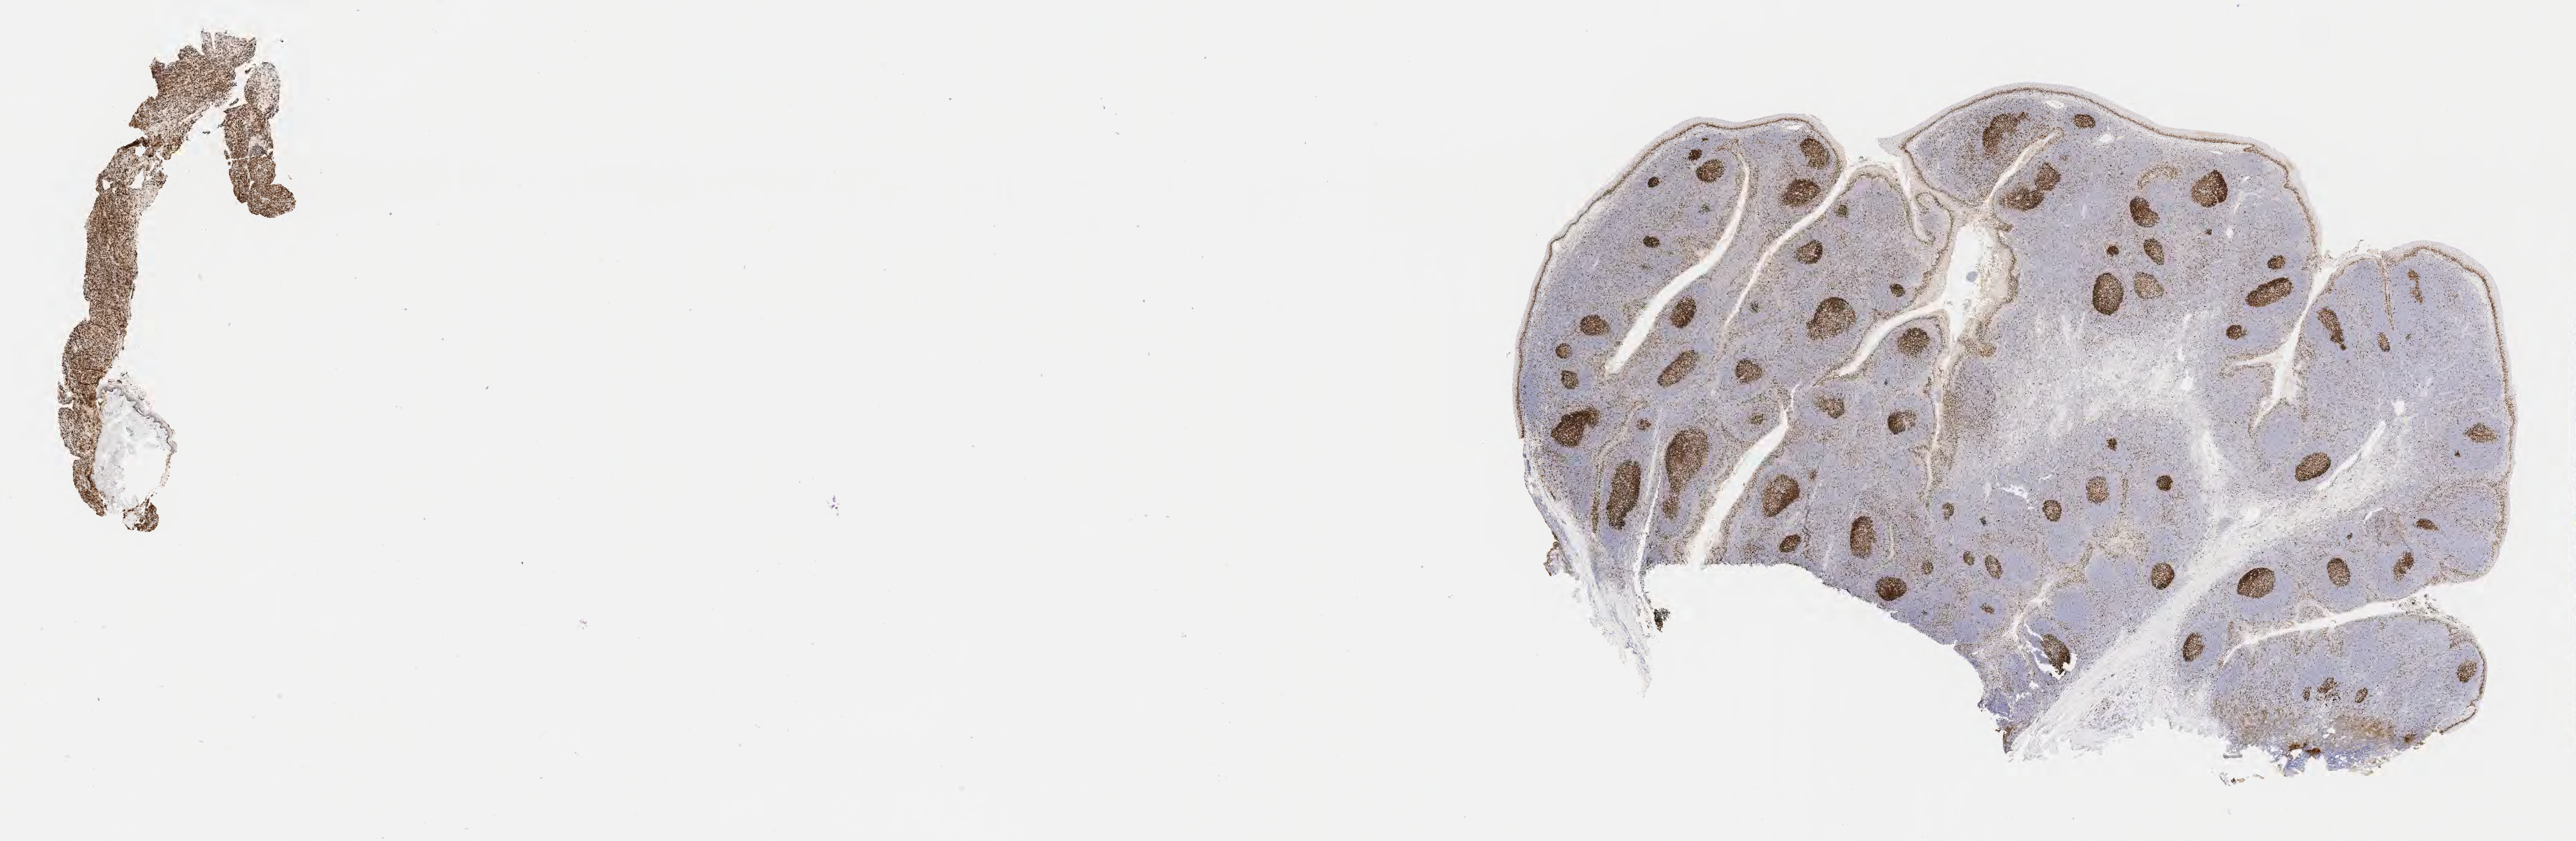
IHC for Ki-67, whole-slide image, low-resolution overview of the scanned area, about 32.2 x 10.5 mm, tumor tissue. Female patient, age 43 years.
Diagnosis: Diffuse large B-cell lymphoma, NOS.